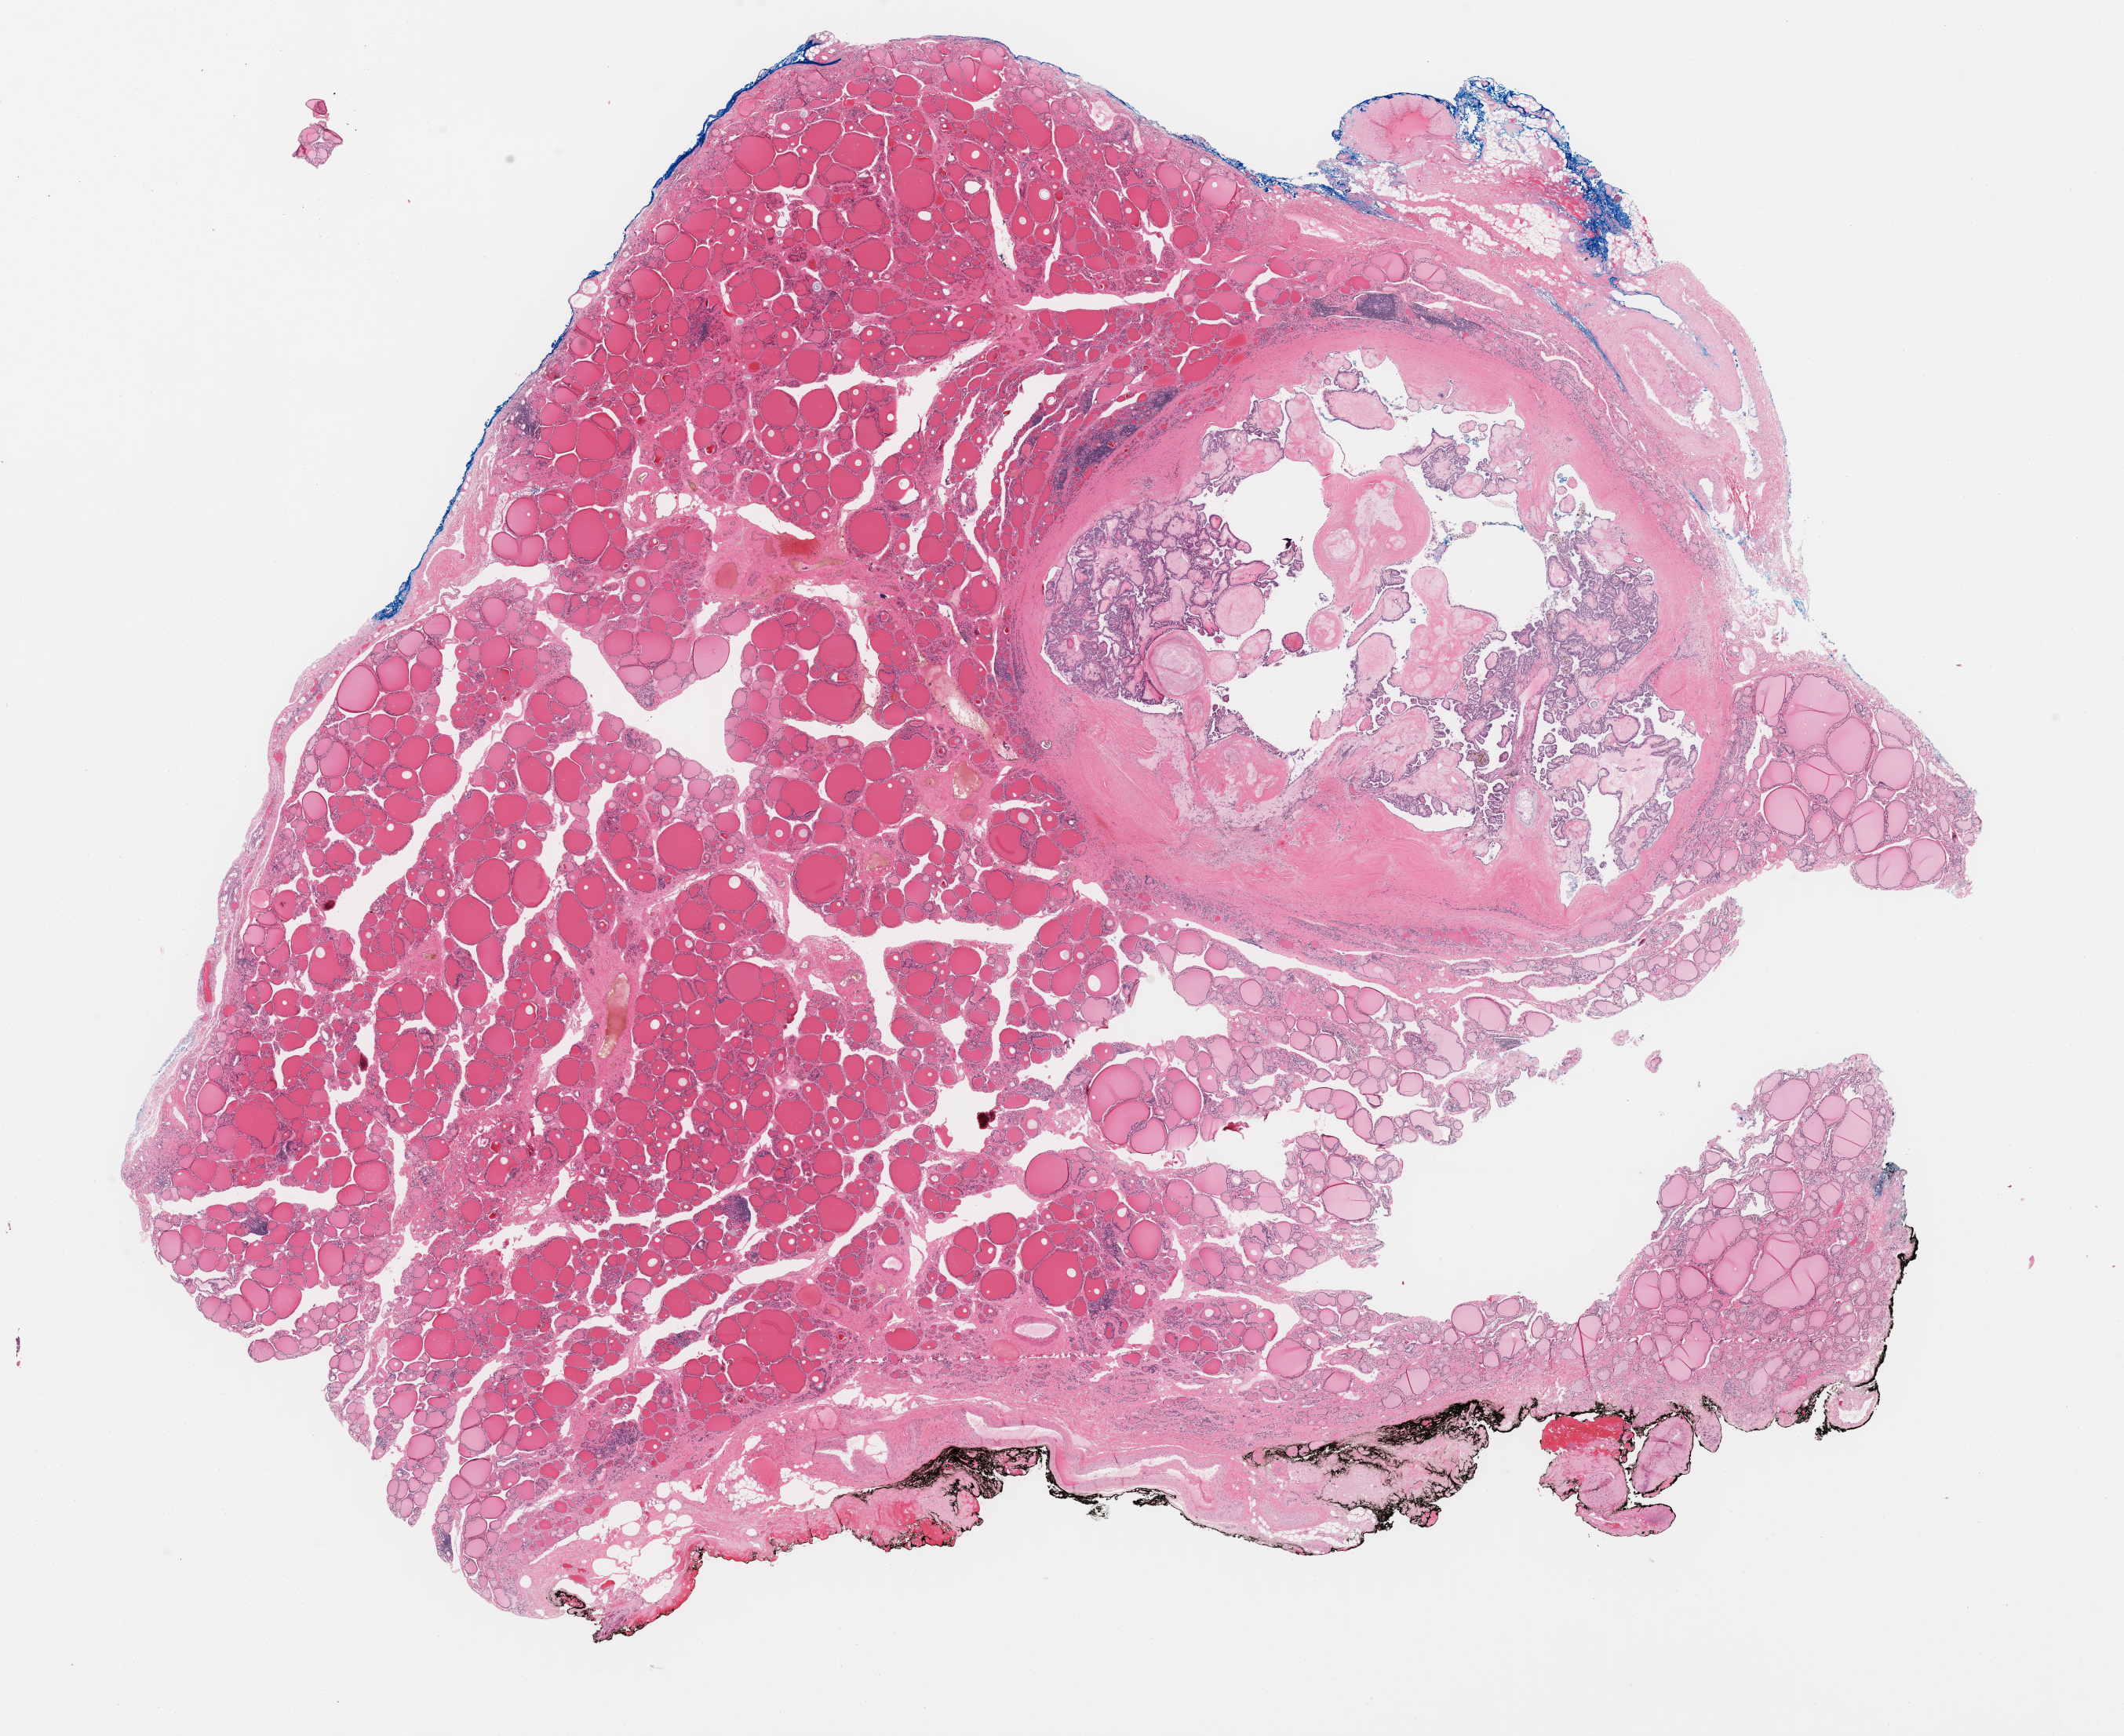
Digitized H&E tissue section (whole slide), shown as a low-resolution overview of the whole scanned area (about 21.4 x 17.5 mm); formalin-fixed paraffin-embedded (FFPE) diagnostic section; sample: primary tumour, thyroid. Female patient; age at initial diagnosis 50 years.
Pathologic diagnosis: Papillary adenocarcinoma, NOS (thyroid gland).